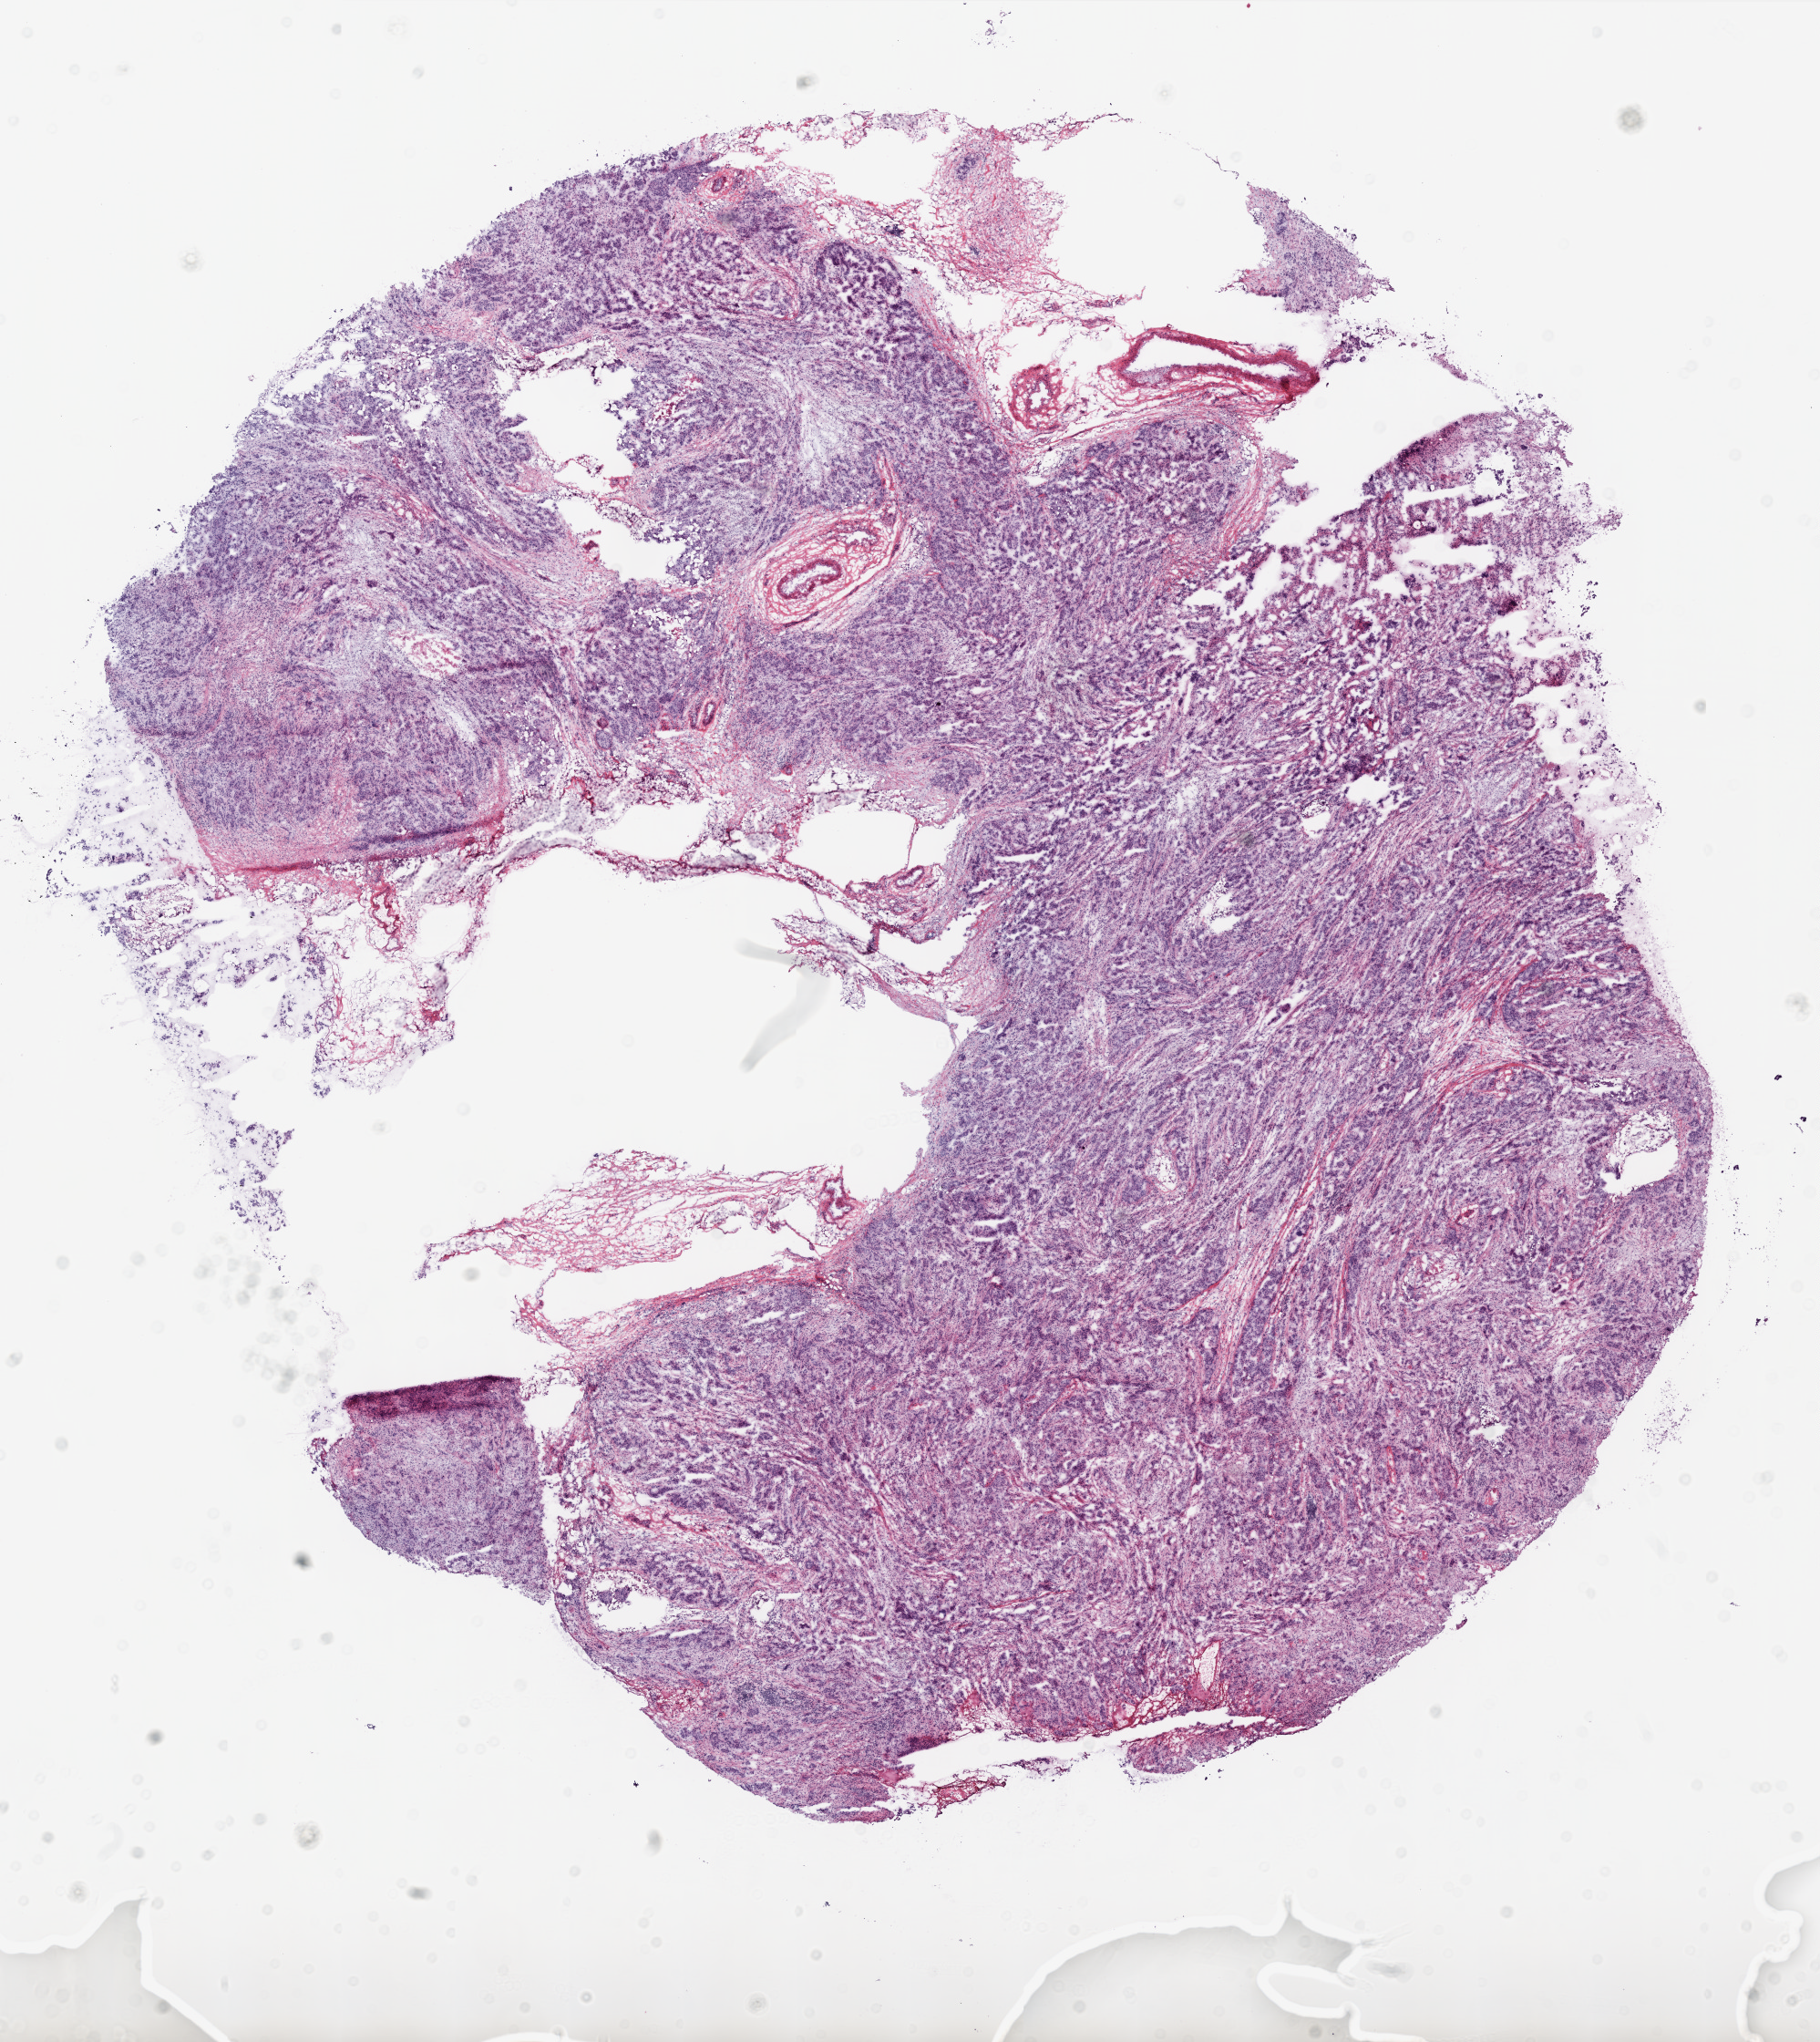
Digitized Hematoxylin and eosin (H&E) stained tissue section (whole slide) — shown as a low-resolution overview of the whole scanned area (about 16.0 x 17.9 mm). Frozen section from the top of the tissue portion. Primary tumour sample from the ovary. Female, age 56 years at initial diagnosis. Histologic grade: G3 (poorly differentiated). Pathologist review of this section (percent, as recorded): tumour cells 75%, tumour nuclei 80%, normal cells 20%, stromal cells 0%, necrosis 5%.
Laterality: bilateral. Diagnosis: Serous cystadenocarcinoma, NOS. FIGO stage: IIIC.